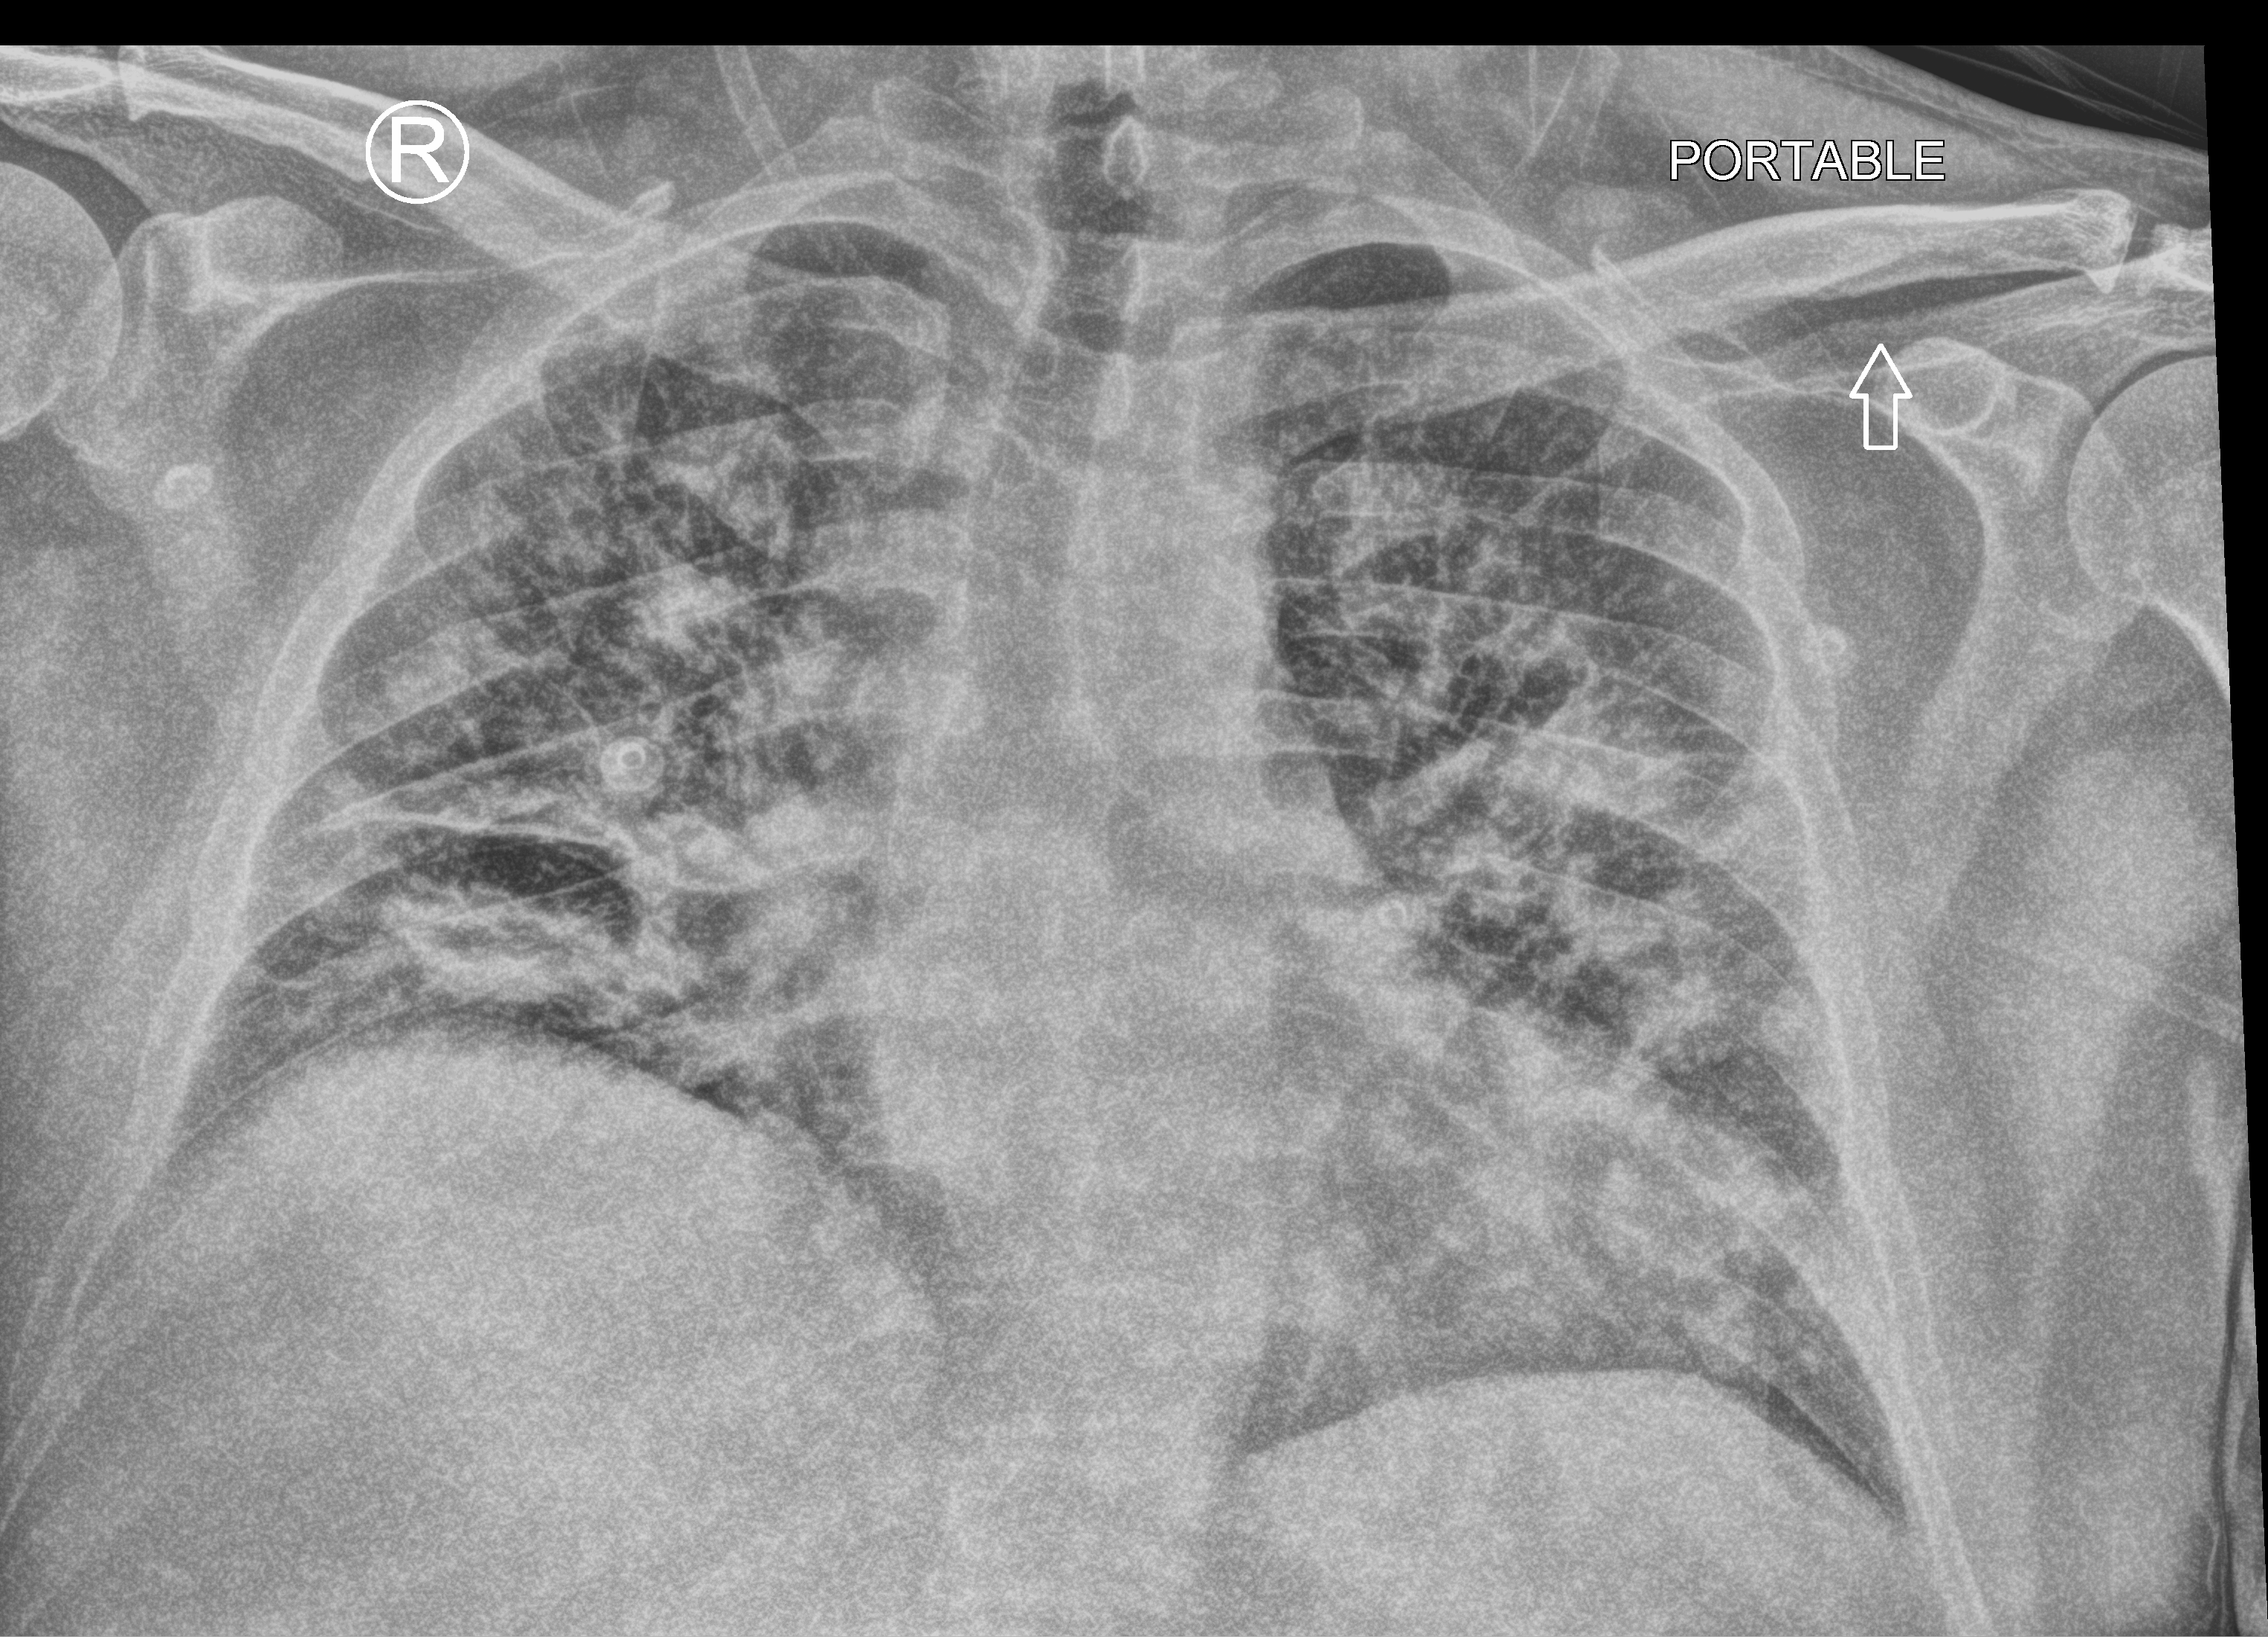
Chest X-ray (portable); anteroposterior (AP) projection. Patient hospitalised with COVID-19; male, aged 18–59 years.
Hospital-stay facts (about this admission, not read from this image; timing relative to this image not recorded): mechanically ventilated during this hospital stay: yes; admitted to intensive care during this hospital stay: yes.